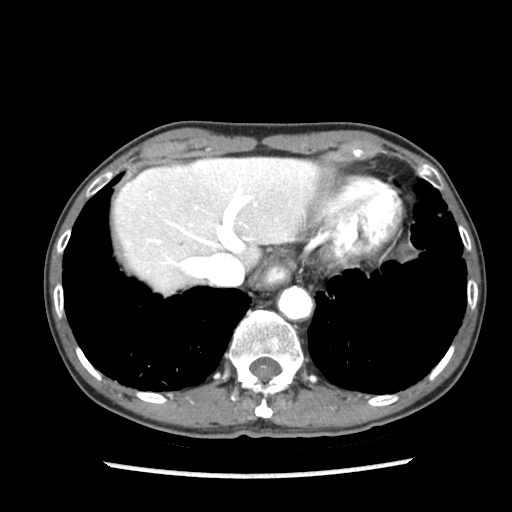
Contrast-enhanced abdominal CT (liver protocol), one axial slice. Slice 70 of 87 in the series (ordered by position). Reconstruction kernel STANDARD. 140 kVp. Soft-tissue window (W 400 / L 40 HU). 2.5 mm slice thickness. 512 × 512 image matrix, field of view 300 × 300 mm. Case-level facts recorded for this patient, not image findings: diagnosis: hepatocellular carcinoma (patient treated with transarterial chemoembolisation; whether this scan precedes or follows treatment is not stated here); TNM stage (as recorded): Stage-IIIB; Child-Pugh class: A; tumour differentiation: well differentiated; tumour nodularity: uninodular.
Outlined on this slice (semi-automatic segmentation, software-assisted and operator-edited):
- liver parenchyma outside the tumour (the mass and vessels are separate outlines, so this box may not span the whole liver): bounding box [x1, y1, x2, y2] px = [114, 158, 320, 294]
- mass: [170, 235, 184, 248]
- liver vessels: [153, 162, 262, 271]